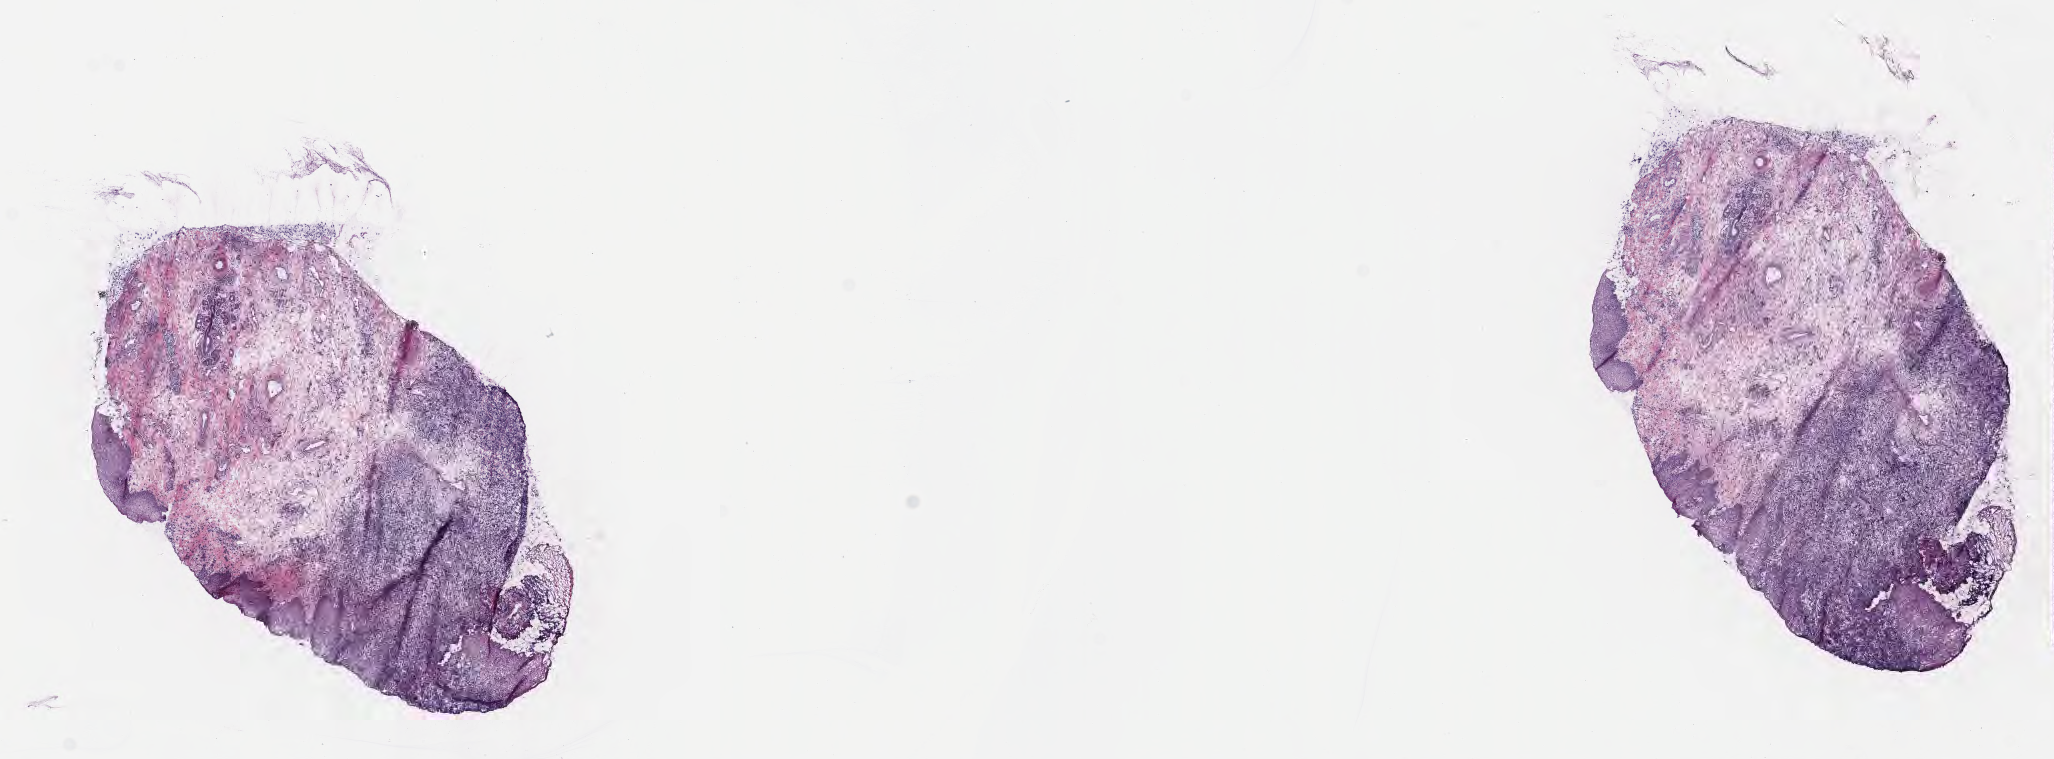
Whole-slide image, haematoxylin and eosin stain, whole scanned area (about 16.6 x 6.1 mm) shown as a low-resolution overview; frozen section (tissue freezing medium); primary tumor; anatomic site: cranium. Female patient; age at initial diagnosis 5 years. Slide review estimates, as recorded: tumor cells 40%, tumor nuclei 70%.
Diagnosis: Burkitt lymphoma, NOS.